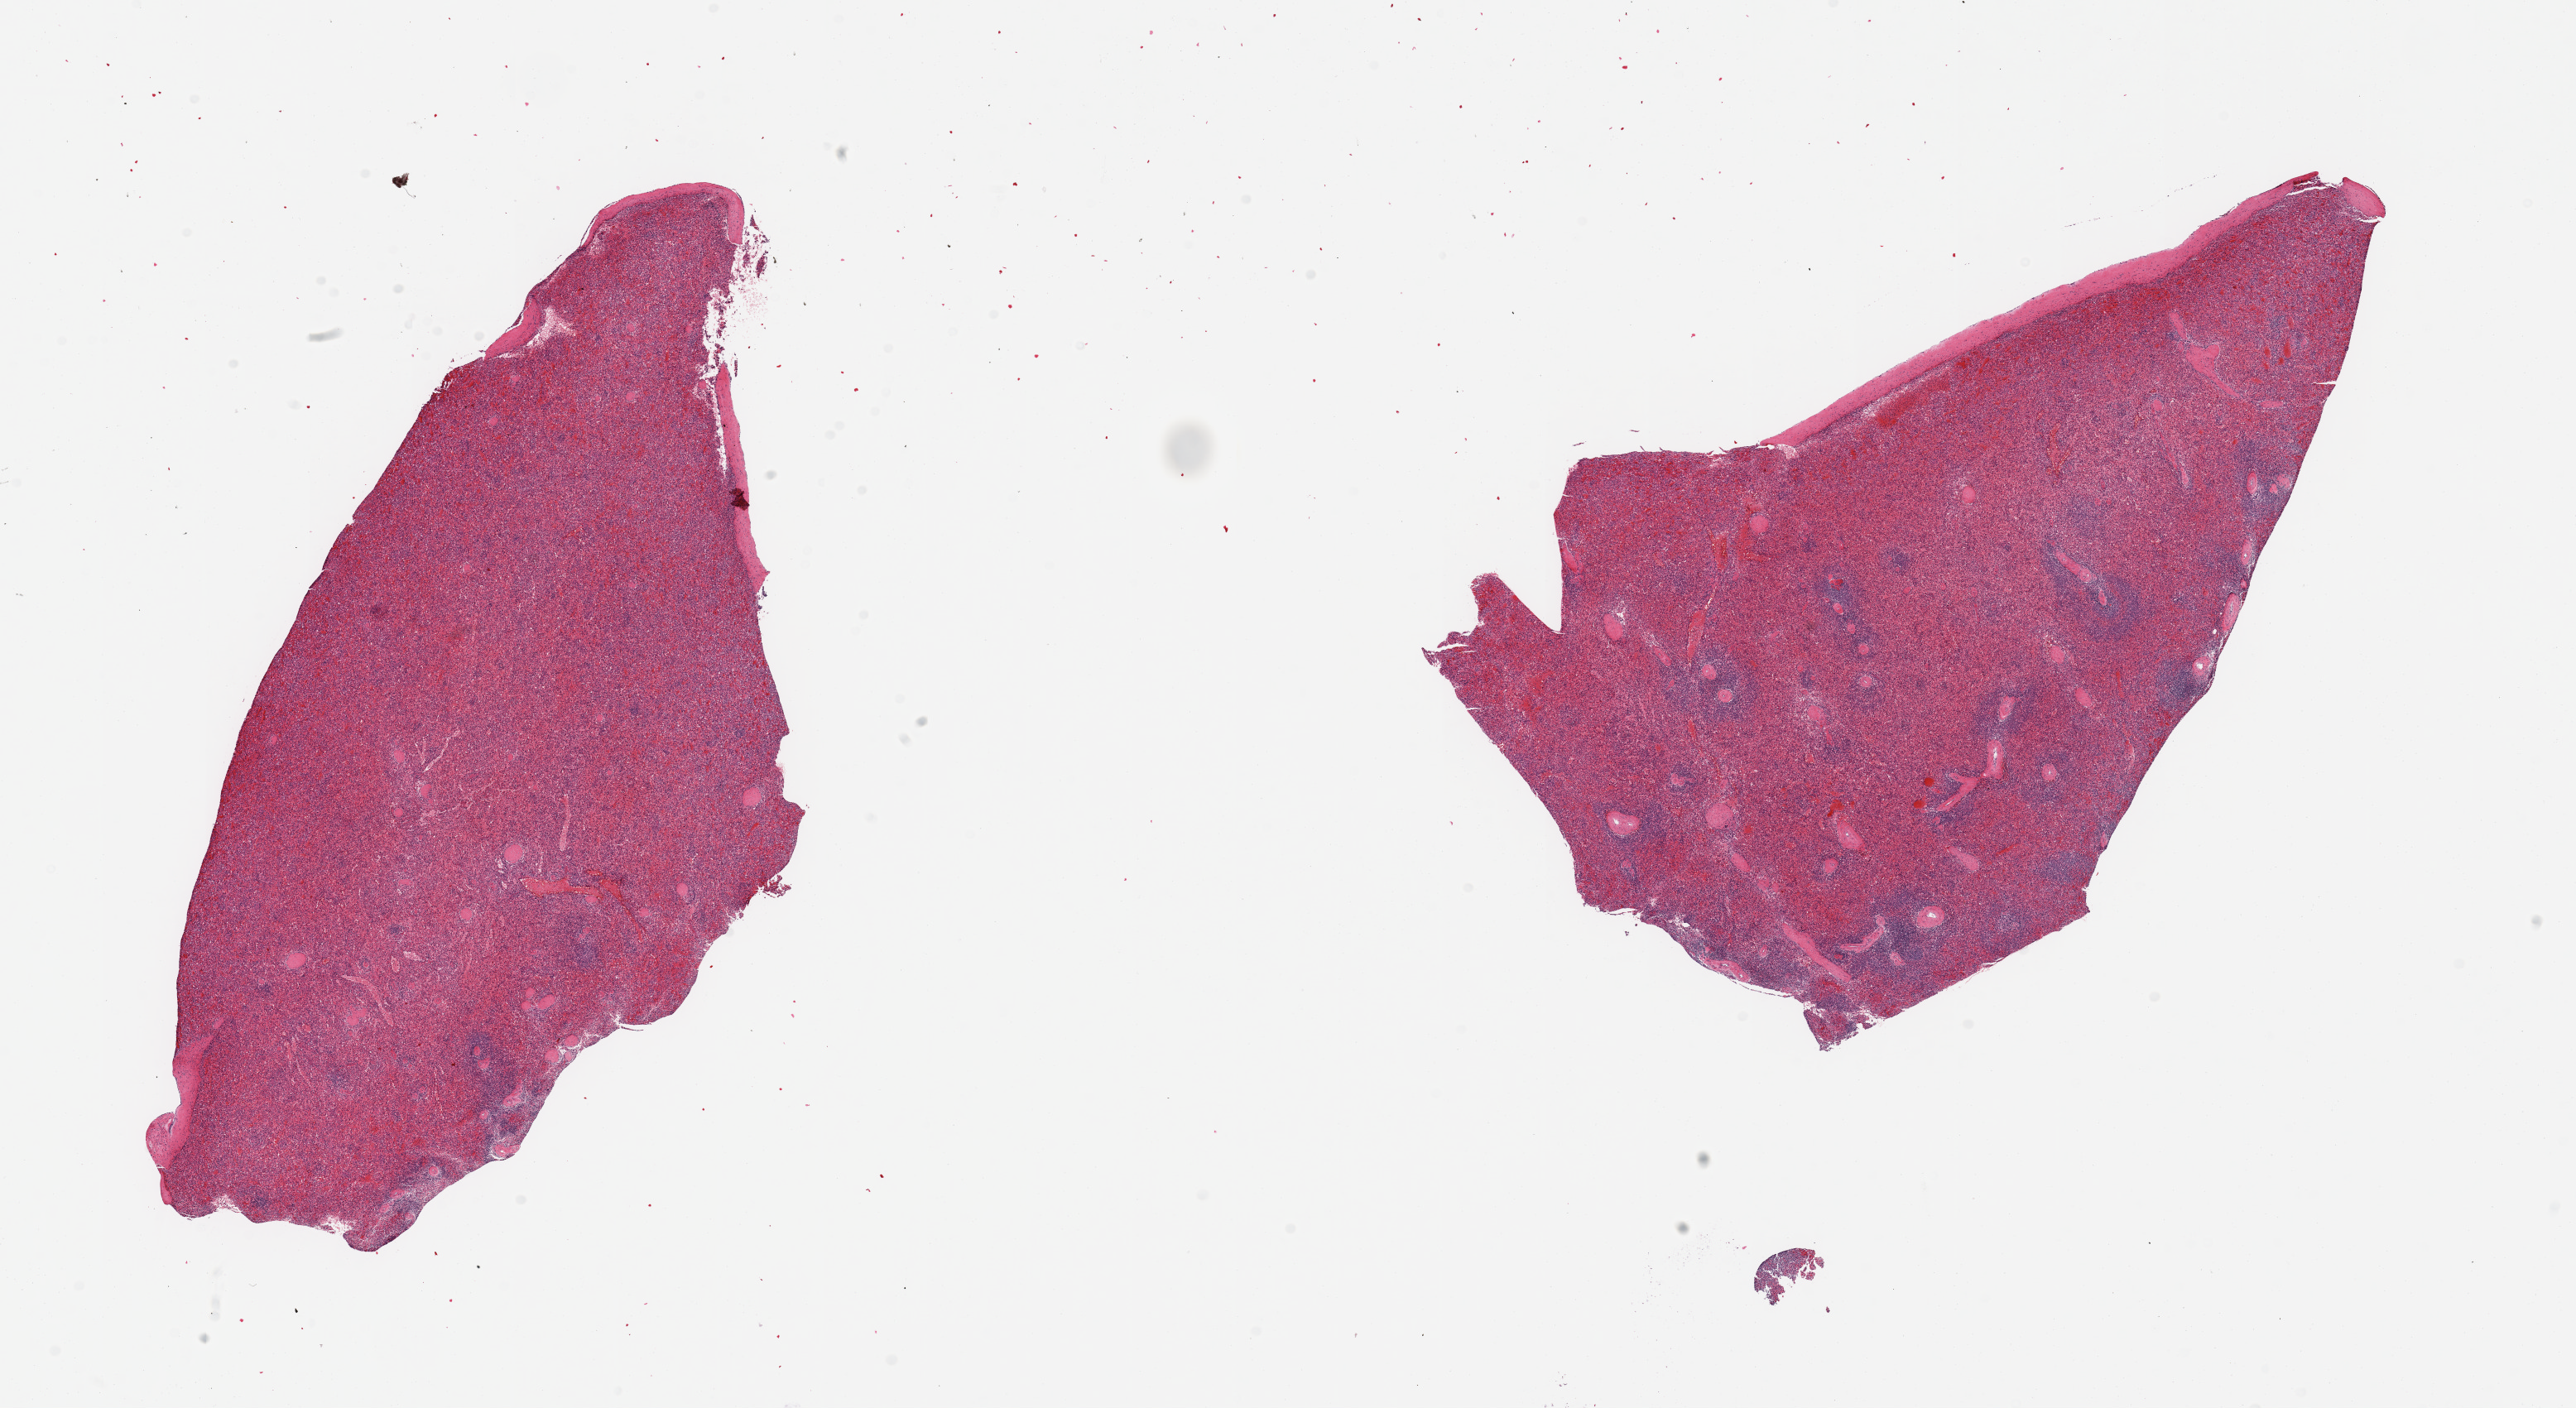
Digitized haematoxylin and eosin-stained section — whole scanned area (about 24.6 x 13.5 mm) shown as a low-resolution overview. PAXgene-fixed, paraffin-embedded tissue. Section of spleen (target tissue). Donor tissue sample. Donor: female.
Pathologist's review note for this sample: 2 pieces; moderate congestion; capsule present.